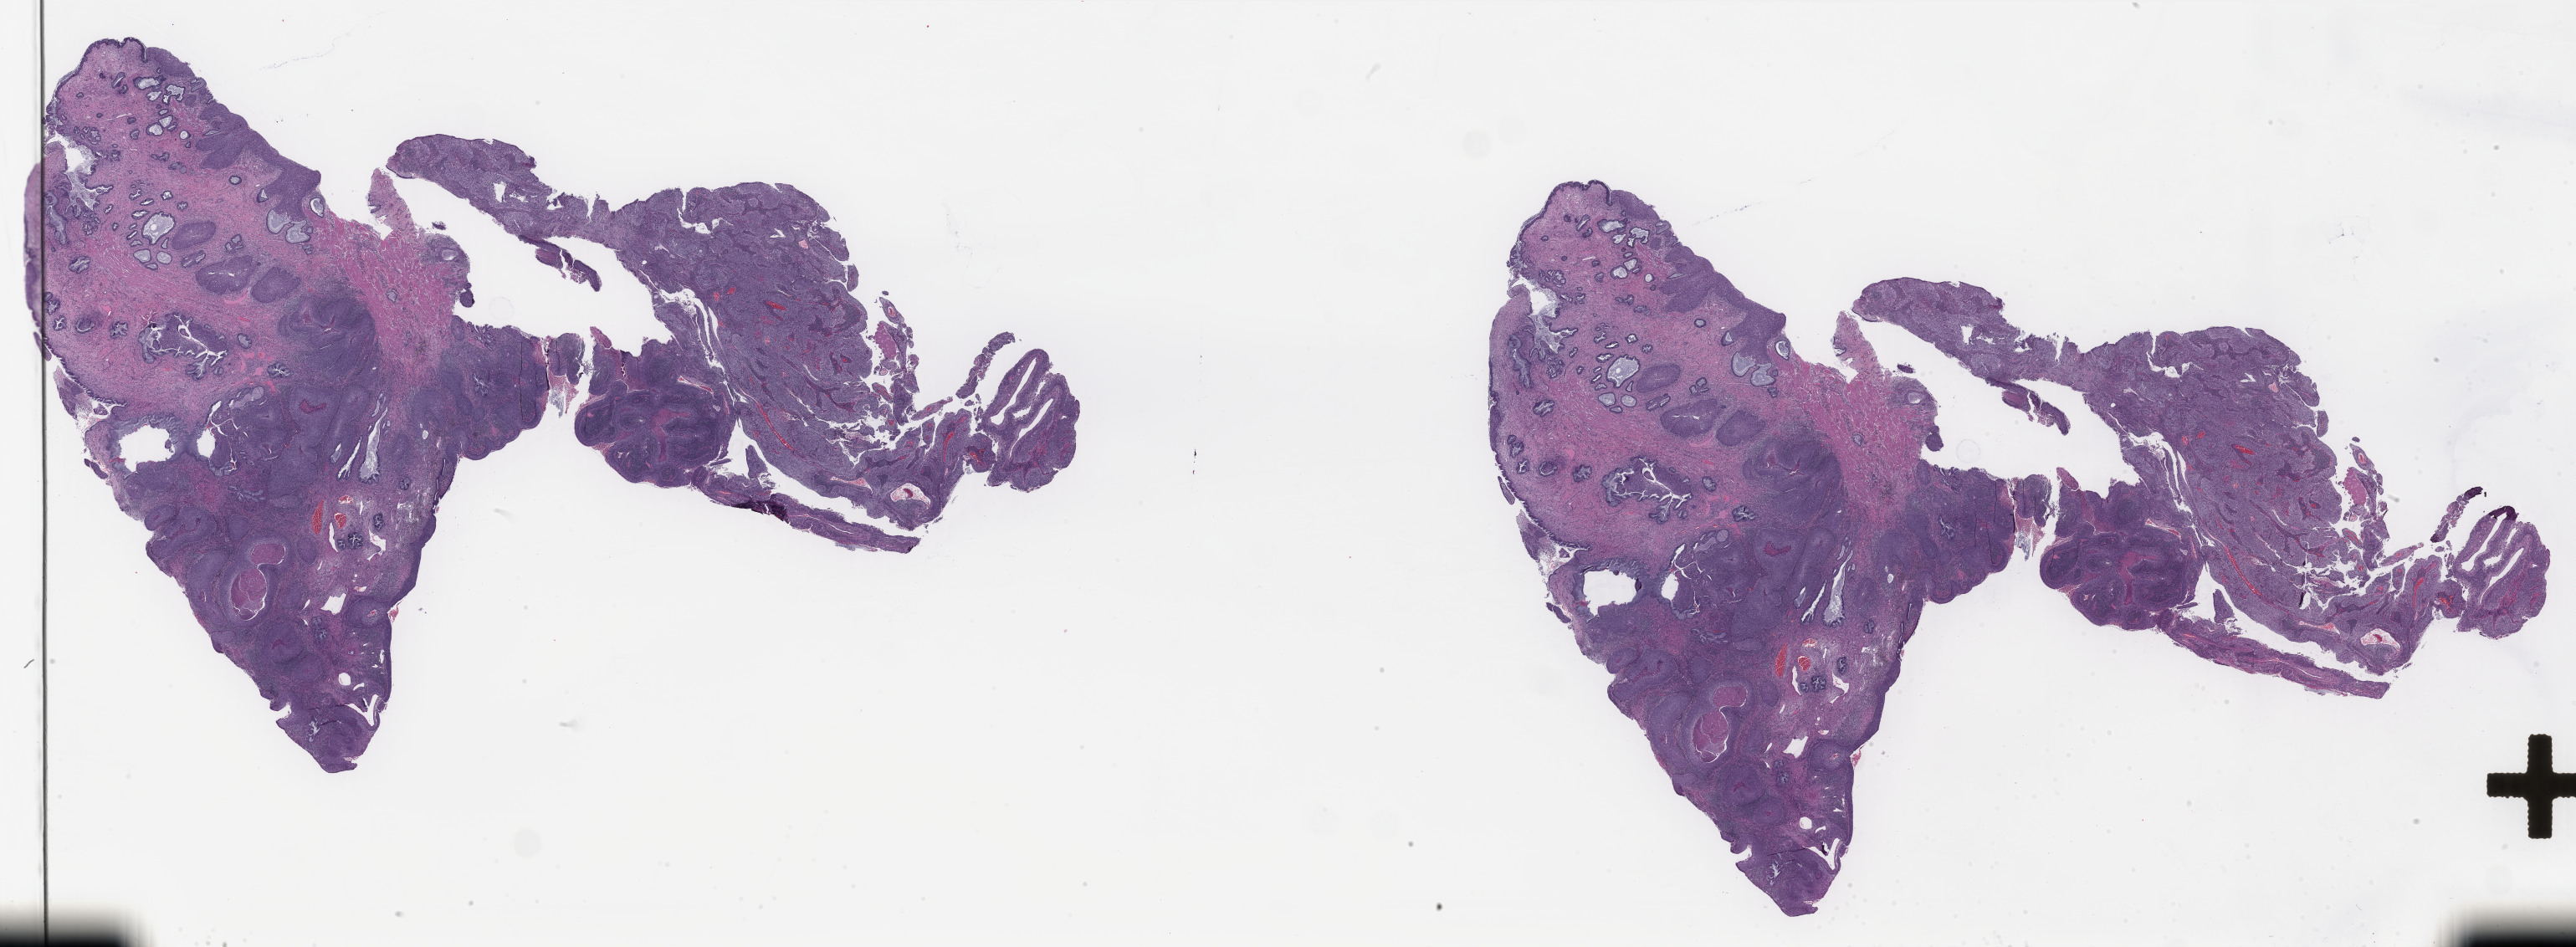
Digitized H&E tissue section (whole slide), a low-resolution overview of the entire scanned area, about 48.7 x 17.9 mm. FFPE section. Cervix, primary tumour sample. Female, age 41 years at initial diagnosis. Histologic grade: G3 (poorly differentiated).
Lymph nodes positive (case pathology): 0 of 26 examined. Diagnosis: Squamous cell carcinoma, large cell, nonkeratinizing, NOS (cervix uteri). FIGO stage: IB1.